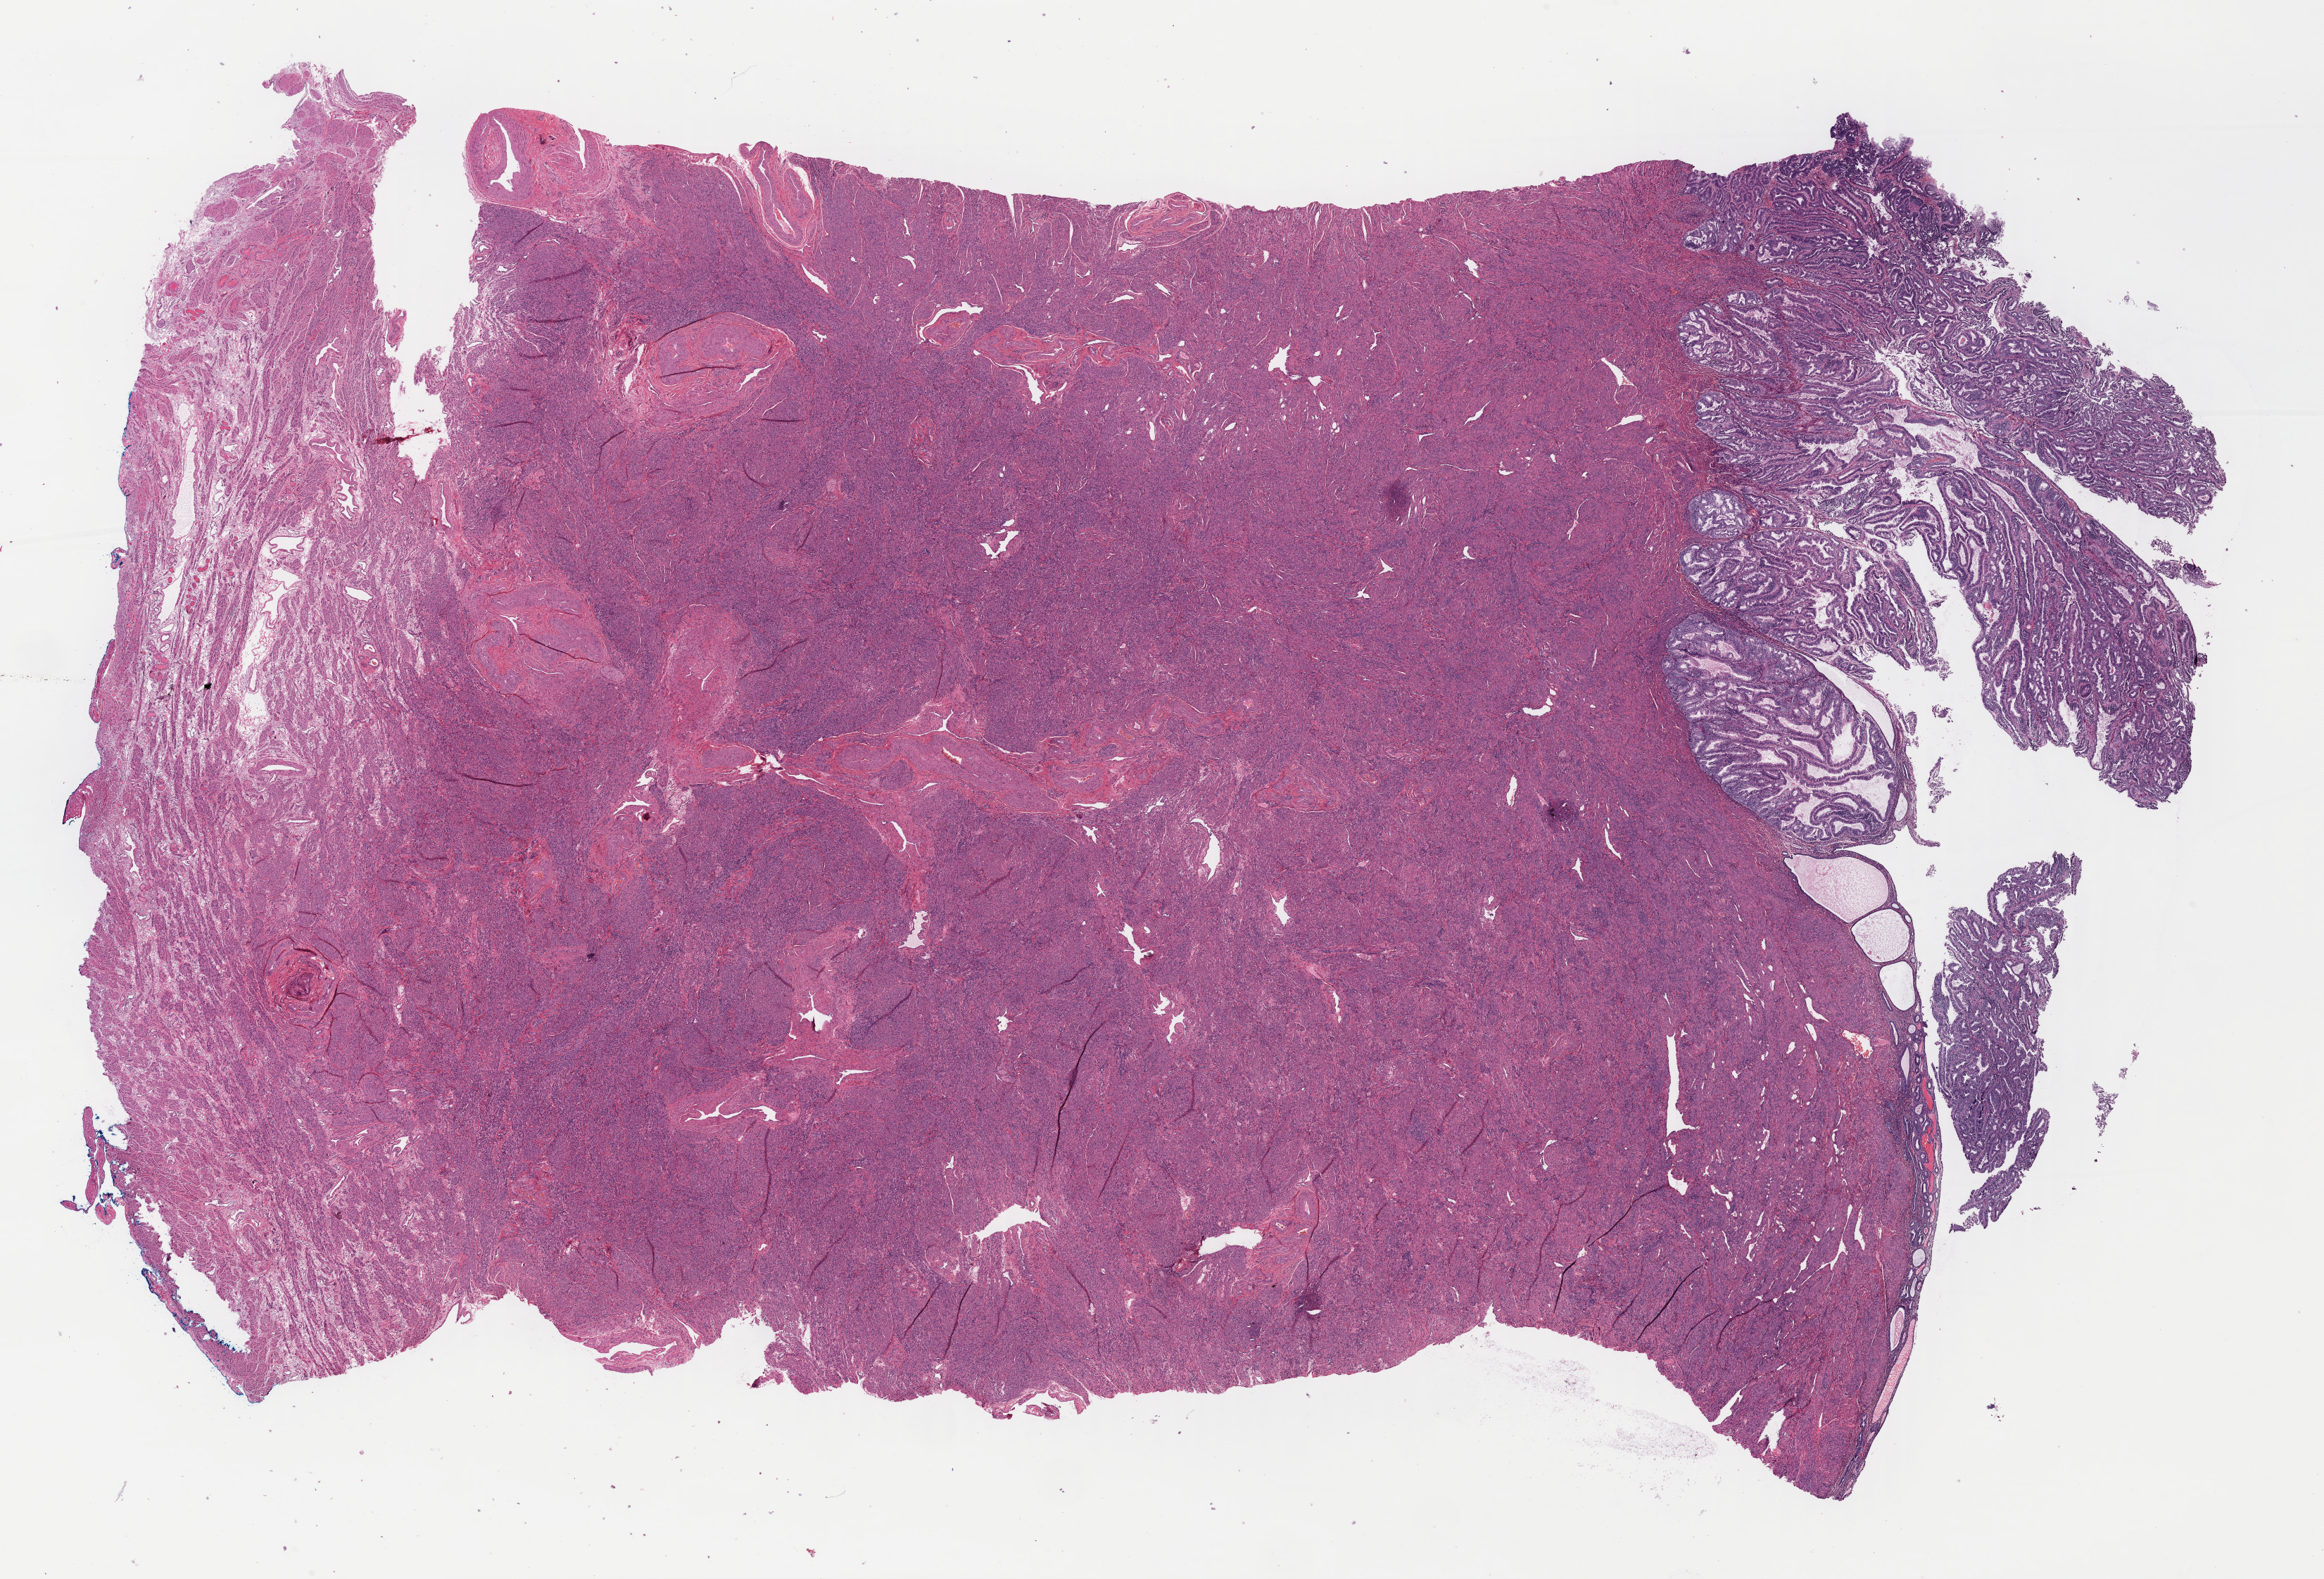
Digitized H&E tissue section (whole slide) — shown as a low-resolution overview of the whole scanned area (about 26.0 x 17.6 mm, slide scanned at 40x); FFPE section; primary tumour sample from the uterus. Patient: female, age at initial diagnosis 55 years. Histologic grade: G1 (well differentiated).
Diagnosis: Endometrioid adenocarcinoma, NOS (endometrium). Lymph nodes positive (case pathology): 0 of 7 examined. FIGO stage: IIIA.